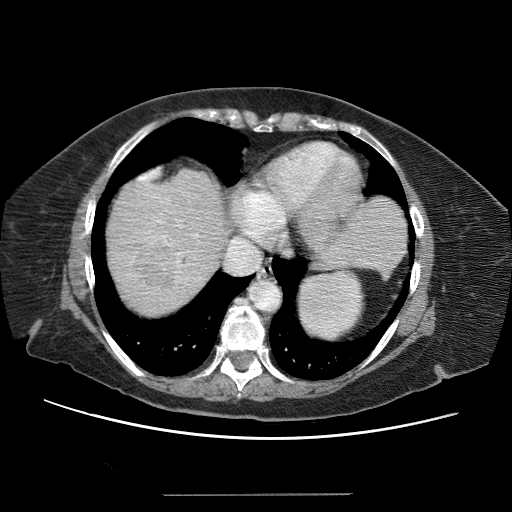
Contrast-enhanced abdominal CT (liver protocol), one axial slice. Position 55 of 65 along the scan axis. 120 kVp. Soft-tissue window (W 400 / L 40 HU). 512 × 512 image matrix, field of view 380 × 380 mm. Case-level facts recorded for this patient, not image findings: diagnosis: hepatocellular carcinoma (patient treated with transarterial chemoembolisation; whether this scan precedes or follows treatment is not stated here); TNM stage (as recorded): Stage-IIIB; Child-Pugh class: A; tumour differentiation: moderately differentiated; tumour nodularity: uninodular.
Outlined on this slice (semi-automatically segmented with operator editing):
- abdominal aorta: bounding box (x1, y1, x2, y2) in pixels: (253, 282, 283, 313)
- liver parenchyma outside the tumour (the mass and vessels are separate outlines, so this box may not span the whole liver): (108, 168, 224, 310)
- mass: (128, 239, 181, 294)
- liver vessels: (113, 173, 215, 296)